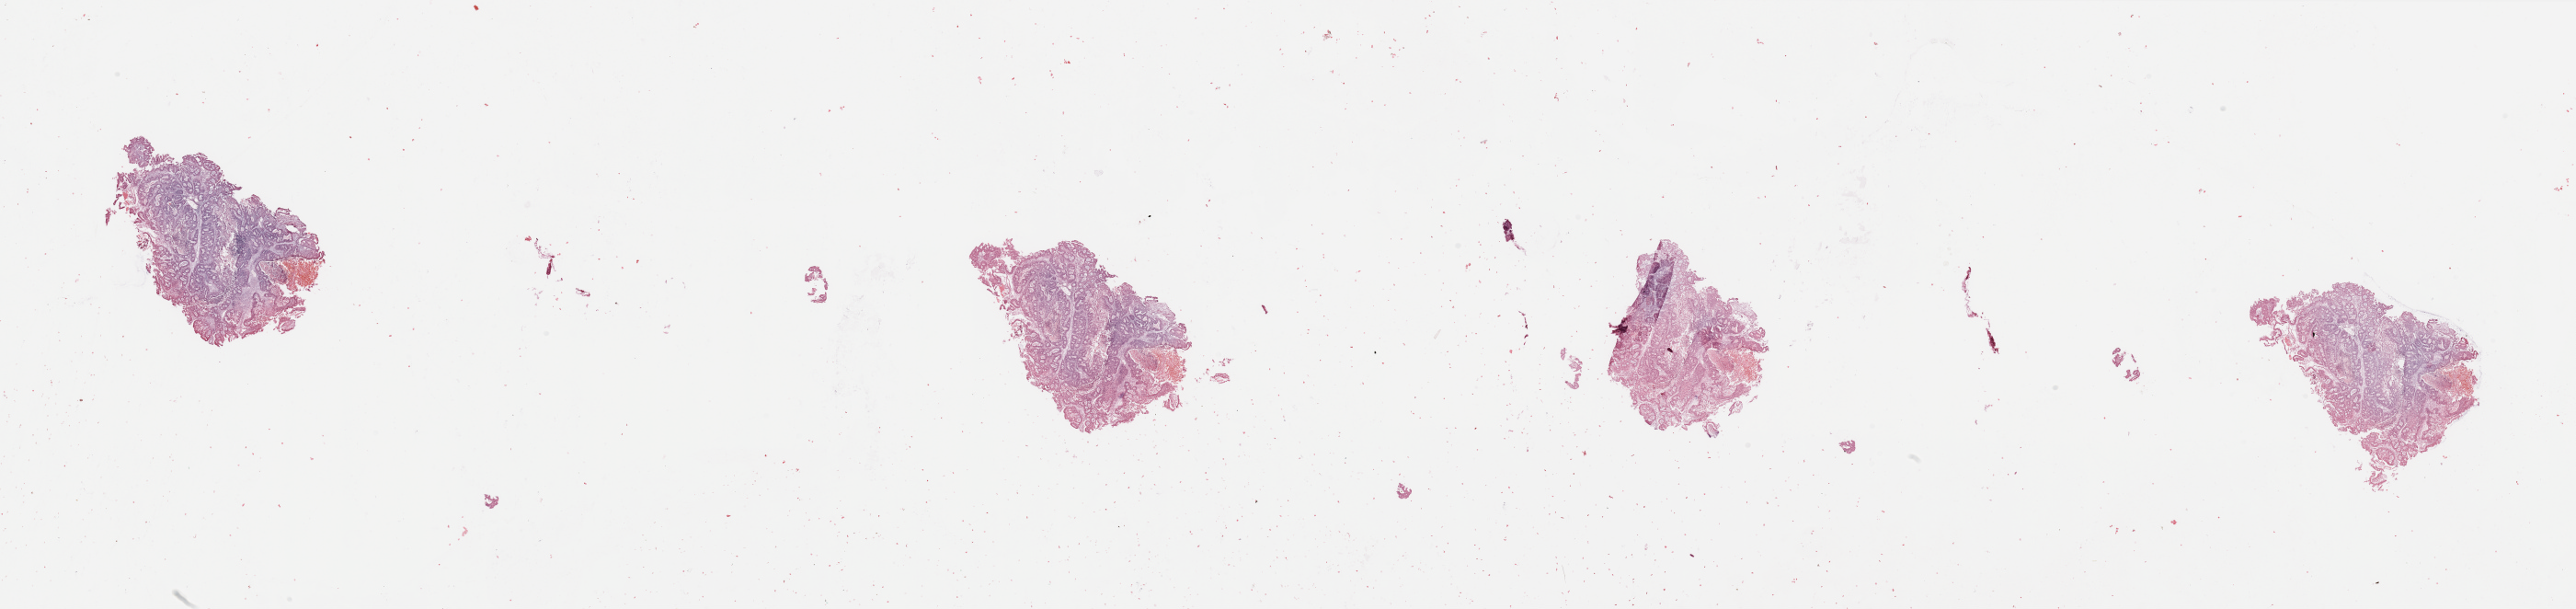
Digitized H&E tissue section (whole slide), shown as a low-resolution overview of the whole scanned area (about 44.3 x 10.5 mm). Tumour tissue sample, sampled site: uterus. 60-year-old female patient.
Histologic diagnosis: Endometrioid adenocarcinoma, NOS.